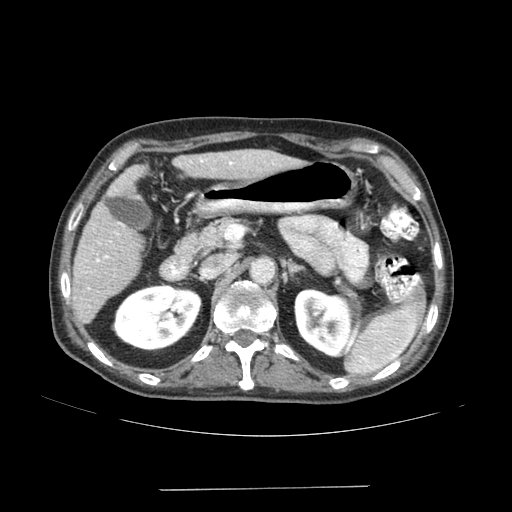
Contrast-enhanced abdominal CT (liver protocol), one axial slice; position 78 of 192 along the scan axis; reconstruction kernel SOFT; 120 kVp; soft-tissue window (W 400 / L 40 HU); 2.5 mm slice thickness; 512 × 512 image matrix. Case-level facts recorded for this patient, not image findings: diagnosis: hepatocellular carcinoma (patient treated with transarterial chemoembolisation; whether this scan precedes or follows treatment is not stated here); TNM stage (as recorded): Stage-IVA; Child-Pugh class: A; tumour nodularity: uninodular.
Outlined on this slice (semi-automatically segmented with operator editing):
- liver parenchyma outside the tumour (the mass and vessels are separate outlines, so this box may not span the whole liver): bounding box <72,150,302,324> (left, top, right, bottom; pixels)
- liver vessels: <96,159,234,262>